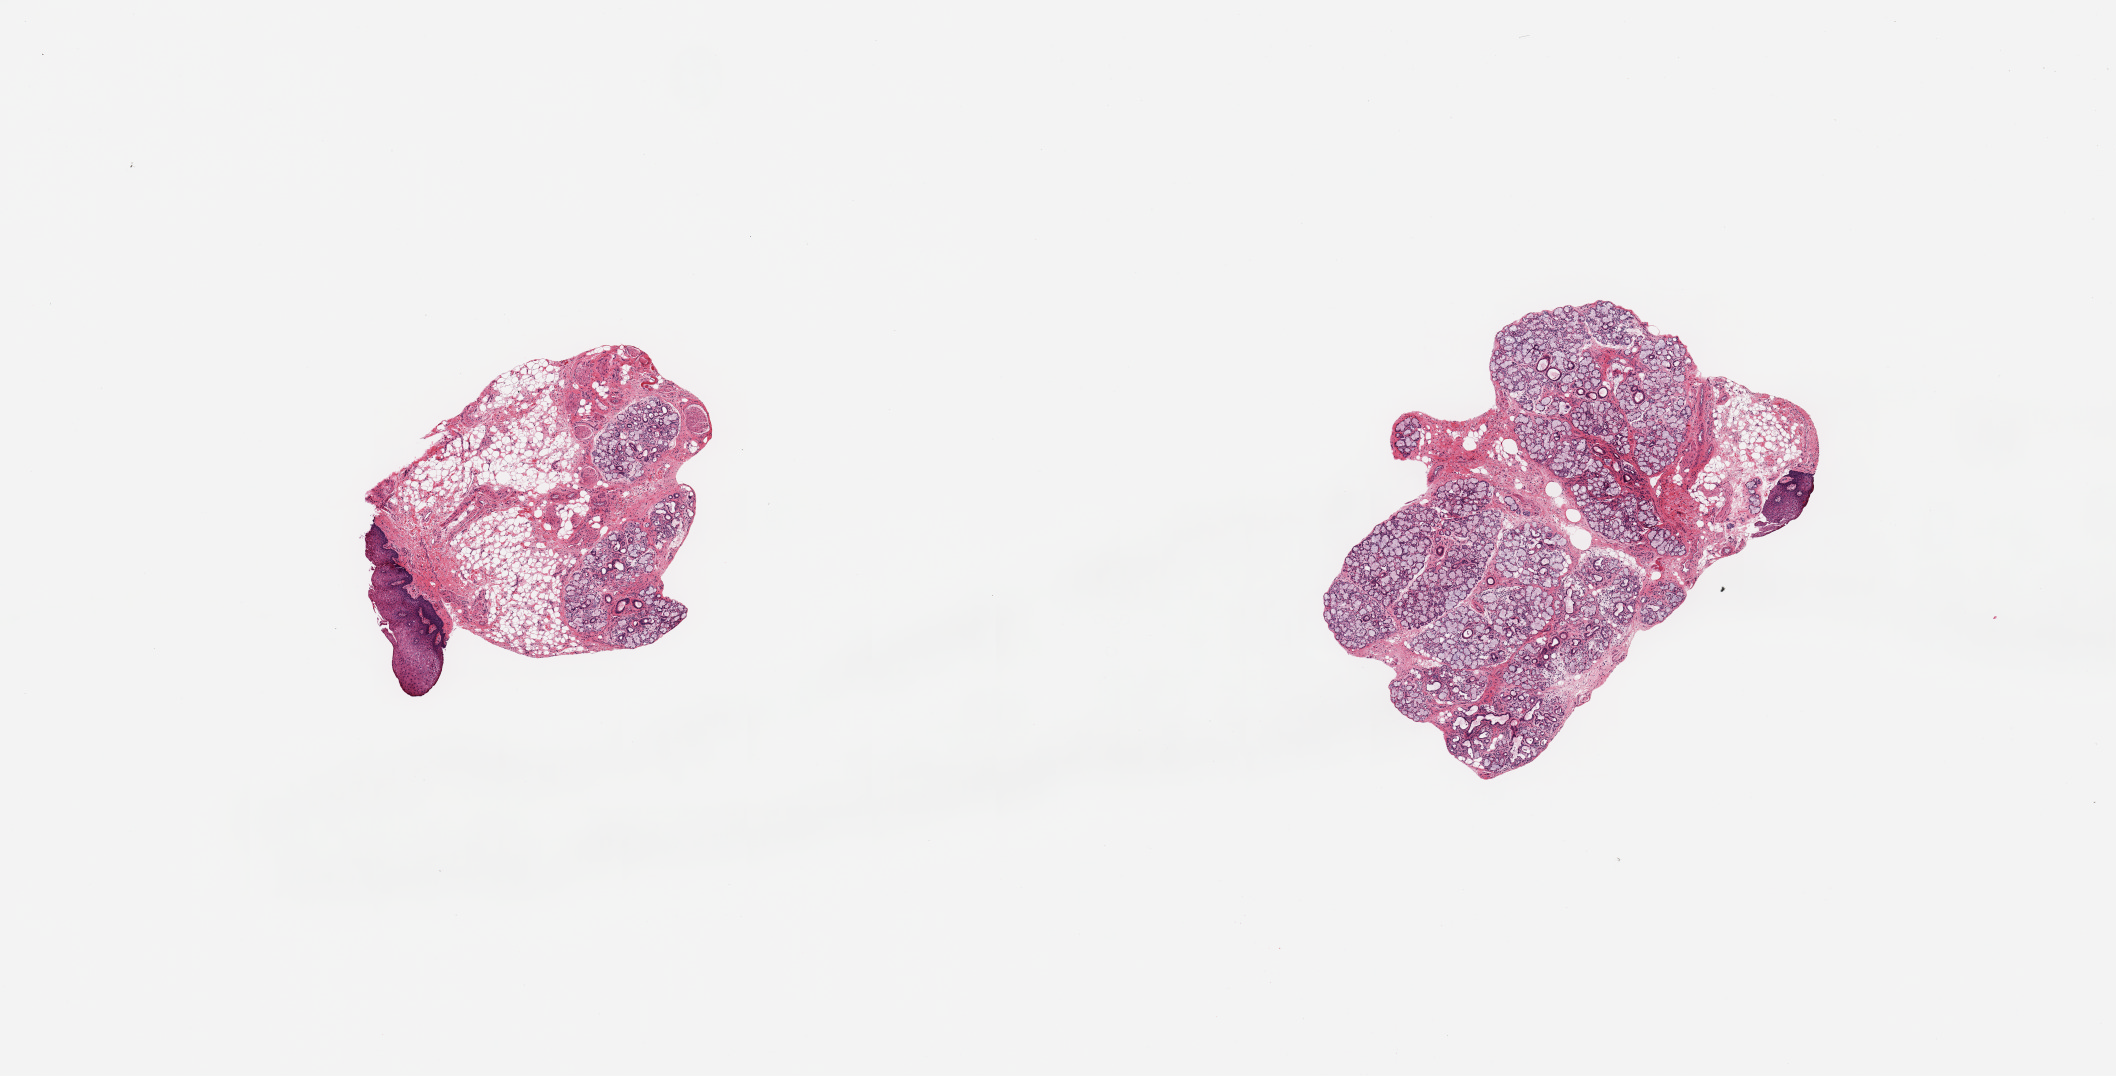
Whole-slide image, haematoxylin and eosin stain, whole scanned area (about 16.7 x 8.5 mm, slide scanned at 20x) shown as a low-resolution overview, PAXgene-fixed, paraffin-embedded tissue, target tissue: minor salivary gland, tissue donor sample. Donor: male.
Review note (as recorded): 2 pieces; 60% lip and fat on 1 piece, 10% on other (both labeled).